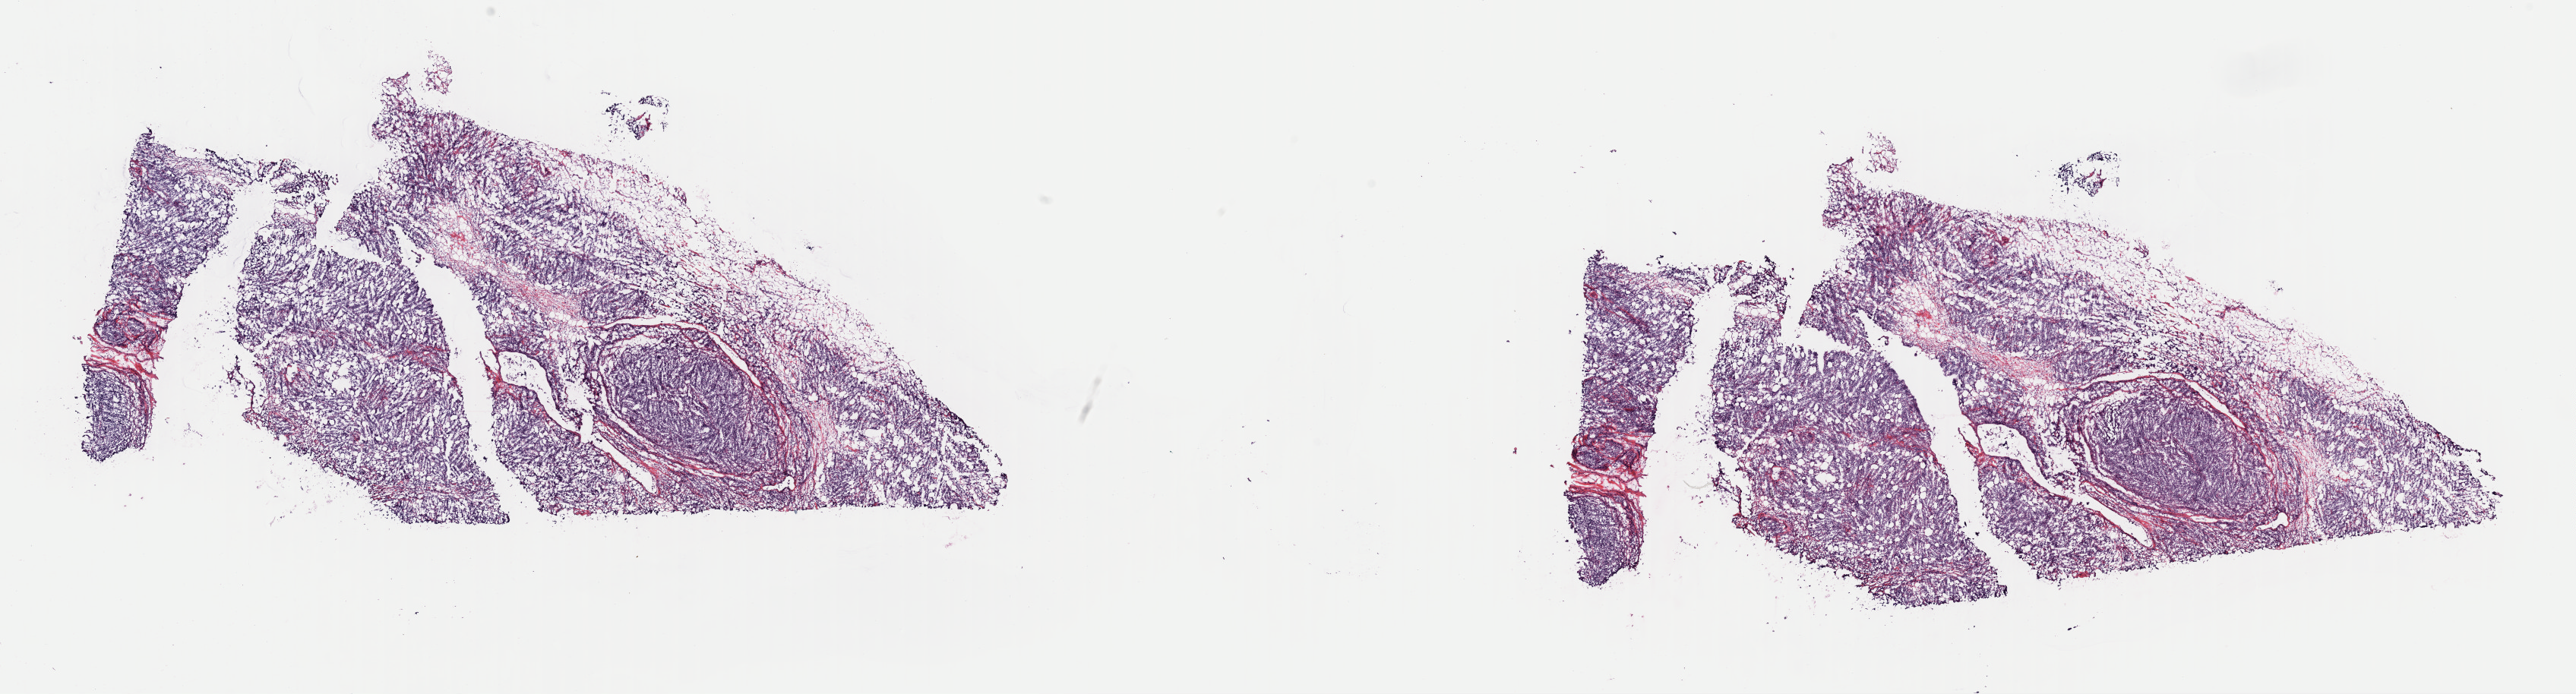
Digitized Hematoxylin and eosin (H&E) stained tissue section (whole slide) — shown as a low-resolution overview of the whole scanned area (about 26.8 x 7.2 mm), frozen section, lymphoid tissue, primary tumour sample. Female patient; age at initial diagnosis 54 years. Slide review estimates, as recorded: tumour cells 80%, tumour nuclei 80%, normal cells 0%, stromal cells 15%, necrosis 5%. Infiltration values recorded for this section: lymphocyte infiltration 80%, monocyte infiltration 5%, neutrophil infiltration 5%.
Pathologic diagnosis: Diffuse large B-cell lymphoma, NOS (breast, NOS).